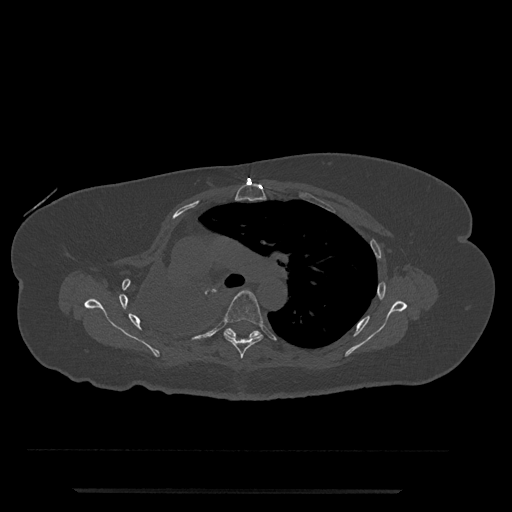
CT including the spine, one axial slice. Slice 530 of 797 in the series (ordered by position). Reconstruction kernel Br40s/3. Bone window (W 1800 / L 400 HU). 0.5 mm slice thickness. 512 × 512 image matrix, field of view 440 × 440 mm. Patient: female, 51 years. From the clinical record (not read from this slice): primary cancer: neuro; vertebrae with lytic lesions (as recorded): T8.
Outlined on this slice (semi-automatic segmentation, software-assisted and operator-edited):
- T5 vertebra: bounding box [x1, y1, x2, y2] px = [224, 290, 263, 359]
- T6 vertebra: [224, 328, 261, 339]